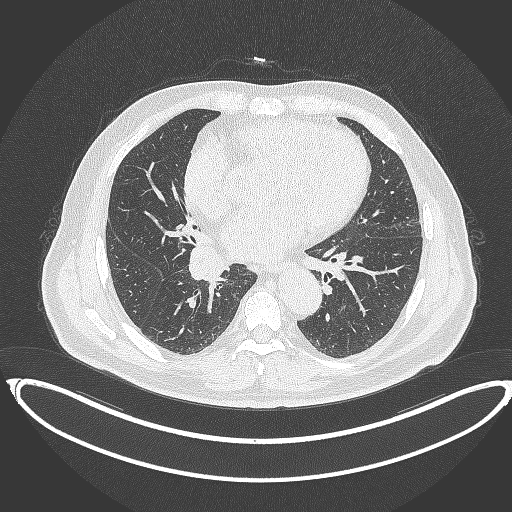
Chest CT, one axial slice. Position 188 of 387 along the scan axis. Reconstruction kernel B70f. 120 kVp. Lung window (W 1500 / L -600 HU). 1 mm slice thickness. 512 × 512 image matrix, field of view 448 × 448 mm. Patient: male, 61 years. From the clinical record (not read from this slice): clinical TNM (as recorded): T1b N1 M0.
Structures marked on this image (rectangle marked by the reading radiologist):
- lung tumour (recorded histology: squamous cell carcinoma): bounding box (x1, y1, x2, y2) in pixels: (188, 241, 230, 284)